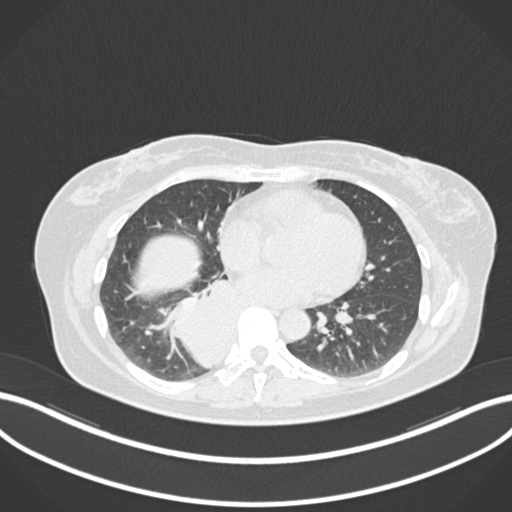
Chest CT, one axial slice. Position 566 of 677 along the scan axis. Reconstruction kernel B30f. 120 kVp. Lung window (W 1500 / L -600 HU). 512 × 512 image matrix, field of view 400 × 400 mm. Female patient, age 54 years. From the clinical record (not read from this slice): clinical TNM (as recorded): T4 N0 M0.
Annotated regions visible in this slice (rectangle marked by the reading radiologist):
- lung tumour (recorded histology: adenocarcinoma): box from (x=158, y=275) to (x=246, y=376) px